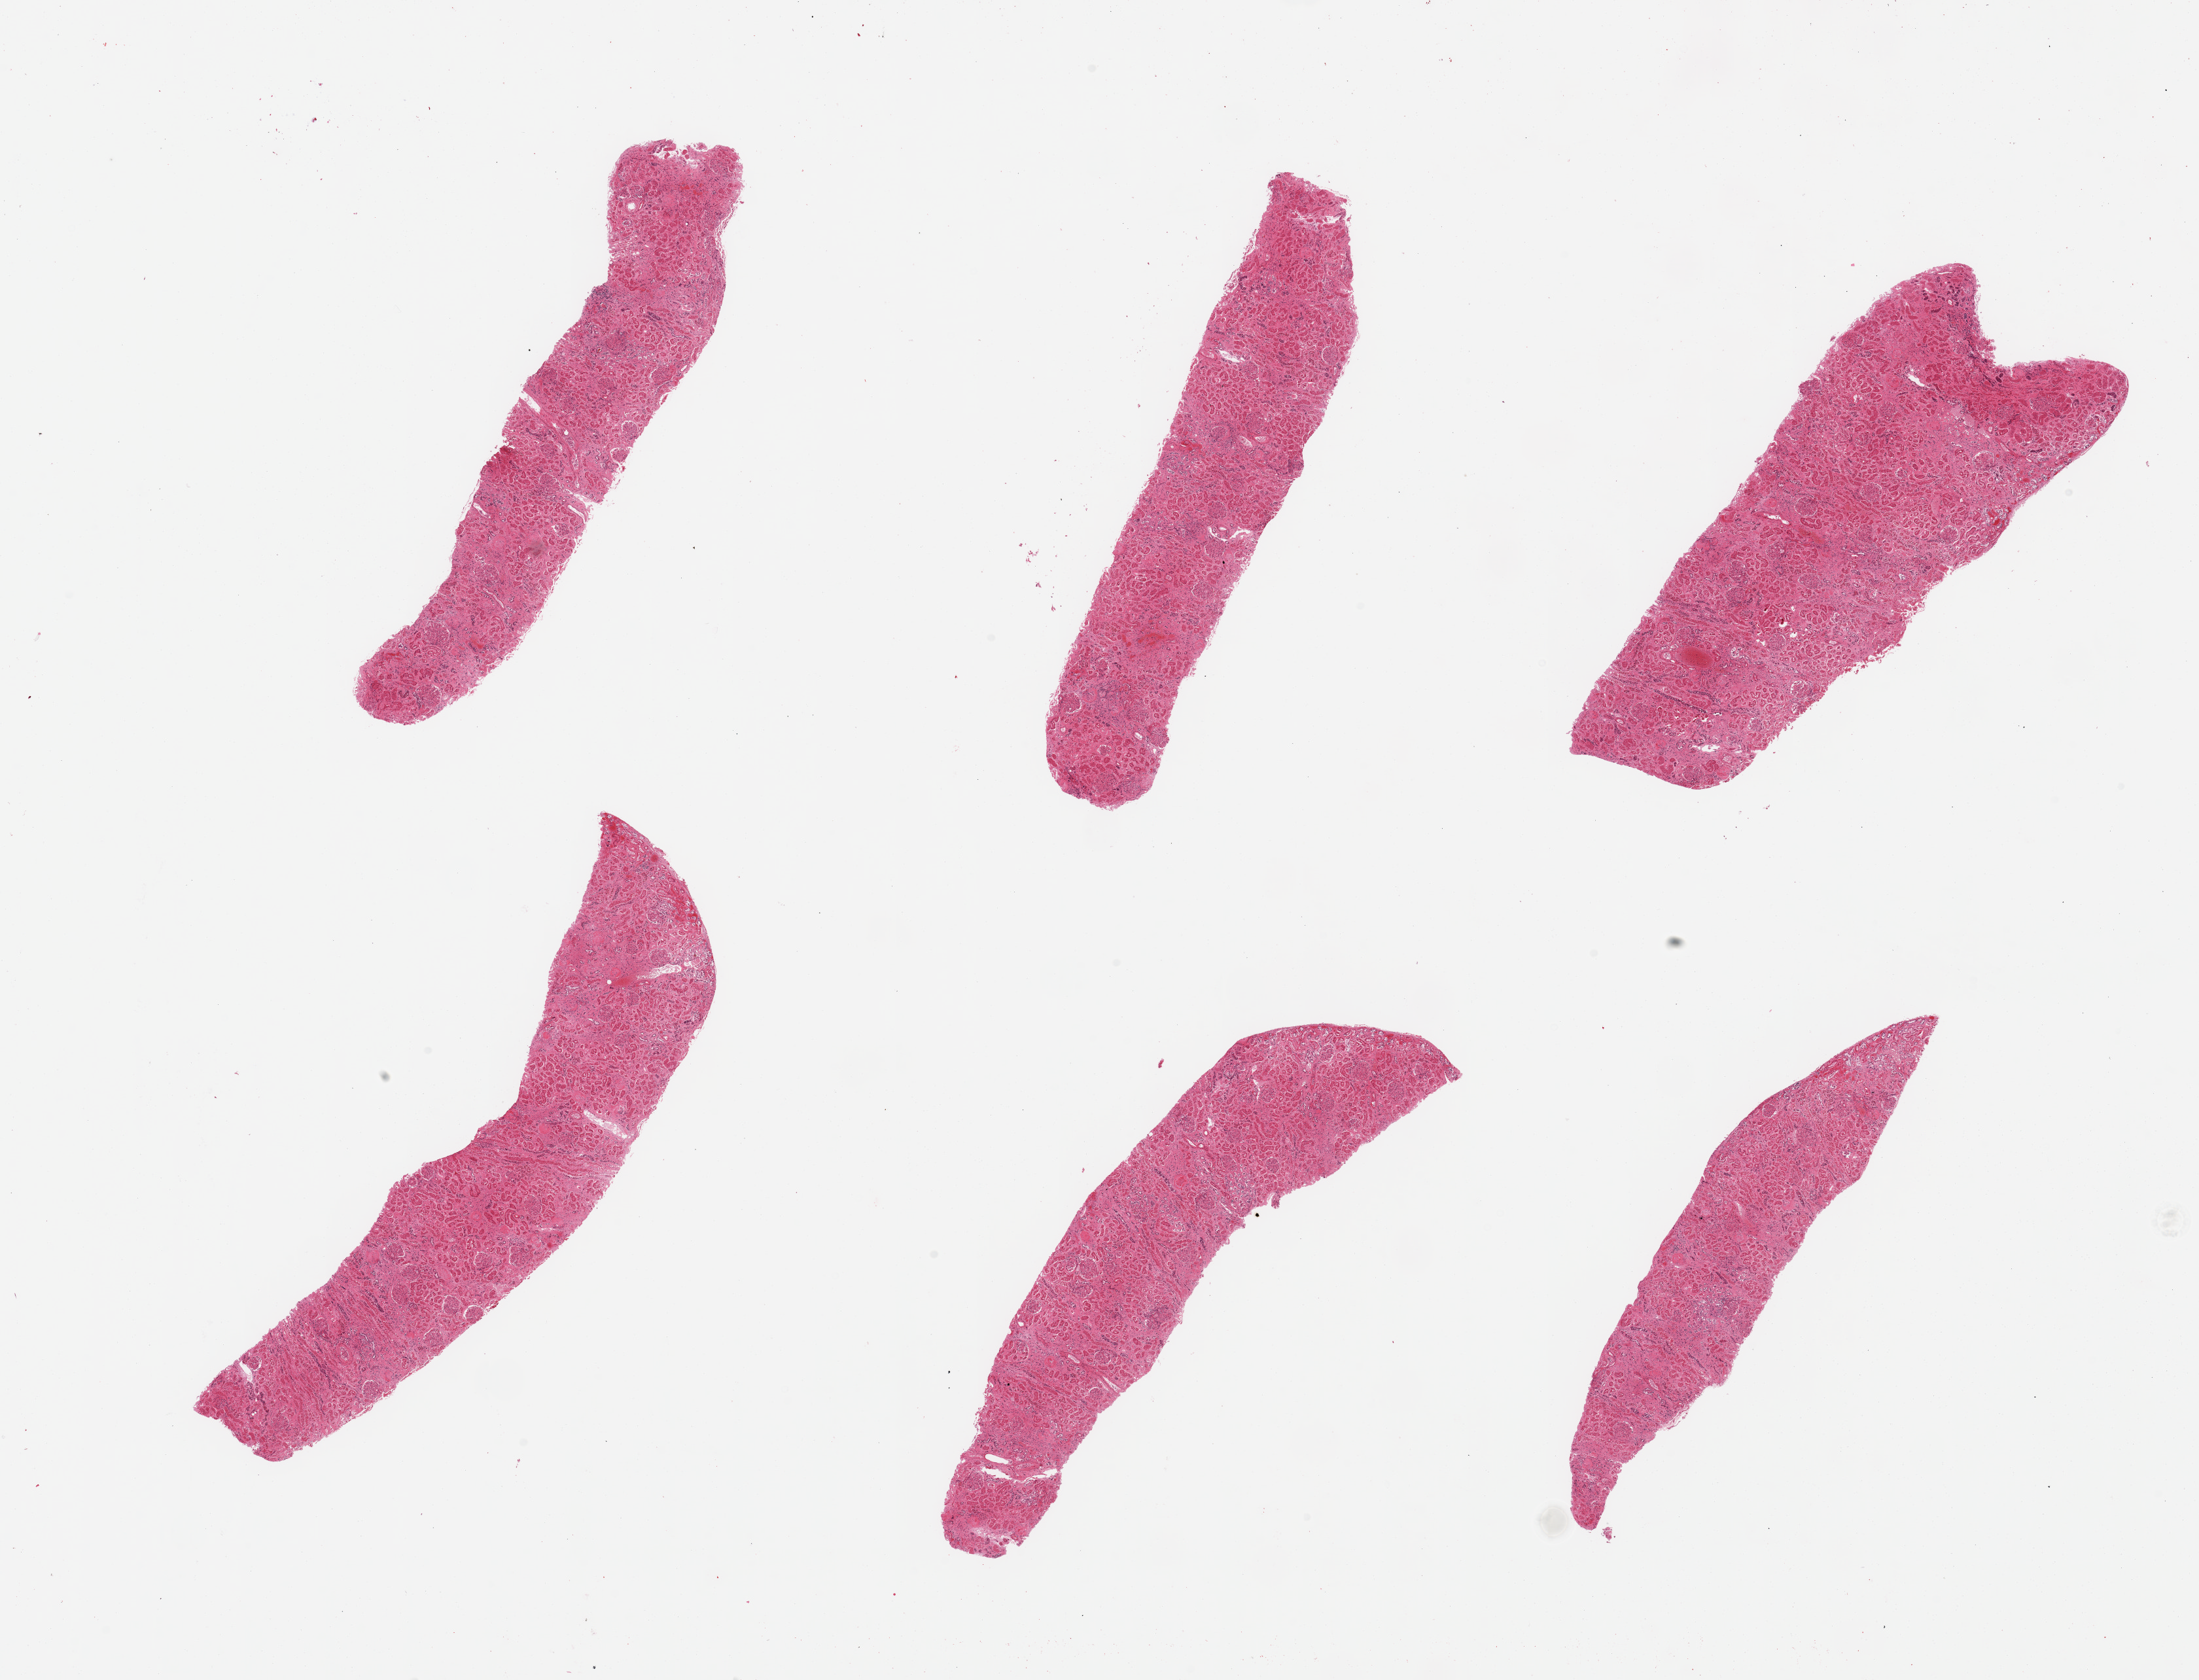
Whole-slide image, hematoxylin and eosin (H&E) stain — low-resolution overview of the scanned area, about 26.6 x 20.3 mm (acquisition: 20x scan), PAXgene-fixed paraffin-embedded (PFPE) section, sampled site (target tissue): renal cortex, tissue donor sample. Donor: male.
- review note (as recorded): 6 pieces, glomeruli present; advanced autolysis